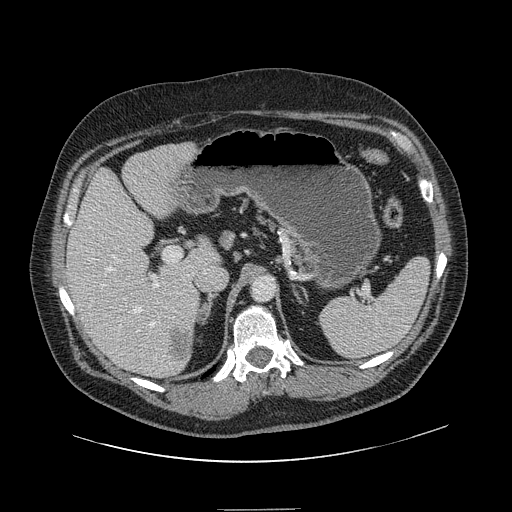
Contrast-enhanced abdominal CT, one axial slice; slice 88 of 154 in the series (ordered by position); 120 kVp; intravenous contrast given; soft-tissue window (W 400 / L 40 HU); 2.5 mm slice thickness; 512 × 512 image matrix. Male patient, age 61 years. From the clinical record (not read from this slice): diagnosis: colorectal cancer liver metastases, imaged before liver resection; multiple liver metastases: yes; largest metastasis: 2.6 cm; disease in both lobes: yes.
Outlined on this slice (manually delineated by an expert):
- hepatic veins: bounding box <89,227,156,360> (left, top, right, bottom; pixels)
- liver: <68,144,217,377>
- planned liver remnant (the part of the liver to remain after resection): <68,147,218,366>
- portal vein (with intrahepatic branches): <102,254,159,288>
- liver metastasis: <170,332,192,364>